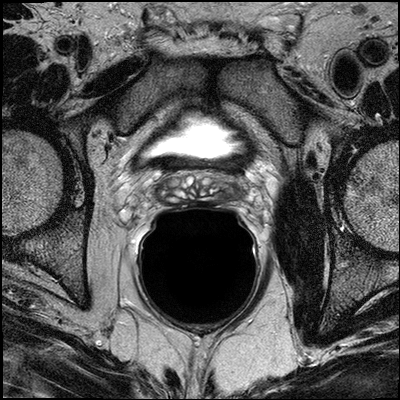
MRI of the prostate; 3 images, each a single mid-volume slice chosen by position (not for content). Treatment context recorded for this patient: Surgery.
Image 1: T2-weighted axial slice, series "T2W_TSE_AX", slice 17 of 32, 3 mm slice thickness.
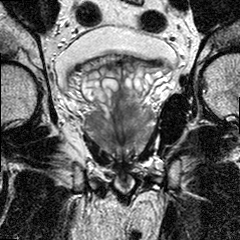
Image 2: T2-weighted coronal slice, series "T2W_TSE_COR", slice 13 of 24, 3 mm slice thickness.
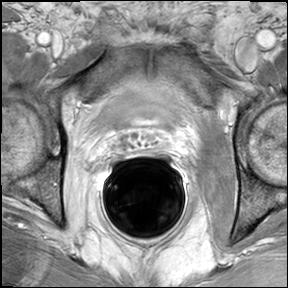
Image 3: DCE (dynamic gadolinium-enhanced) axial slice, slice 17 of 32, dynamic phase 5 of 8.
Report of this MRI examination:
The prostate anatomy is preserved. The central gland shows in the AP age typical heterogeneous signal and nodularity. In the mid 3rd of the prostate, peripheral right peripheral zone posterior lateral between 7 and 9 o'clock there is a geographic hypo intense area seen measuring 1.4 x 1.5 cm, abutting the pseudo capsule, also towards the neurovascular bundle; this mass extends to the base and apex; although there is likely capsular infiltration on the right; there is no tumor mass seen beyond the capsule and the right neural vascular bundle itself seems not to be involved. This area shows suspicious contrast enhancement on the dynamic series. Smaller areas of similar T2 weighted hypo intense signal and suspicious kinetics are seen in the left posterior lateral peripheral zone. No extraglandular extension on the left. No evidence of neural vascular bundle involvement on either side; the seminal vesicles are fluid filled and thin walled without evidence of infiltration. There are no enlarged obturator or internal iliac lymph node seen. The visualized osseous structures are unremarkable. Incidental note is made of a atrophic right obturator muscles and atrophic left psoas major muscle; both are fatty replaced.. IMPRESSION: Imaging findings are suggestive for bilateral prostate cancer with dominant nodule in the right posterior lateral peripheral zone of the mid third of the prostate,between 7 and 9 o'clock, measuring 1.5 cm, in this area capsular infiltration likely. However, no manifest extracapsular disease visualized. No evidence of neural vascular bundle involvement on either side. No seminal vesicle infiltration. No pelvic lymphadenopathy. The visualized osseous structures are unremarkable. Incidental note is made of an atrophic right obturator and left psoas muscles.